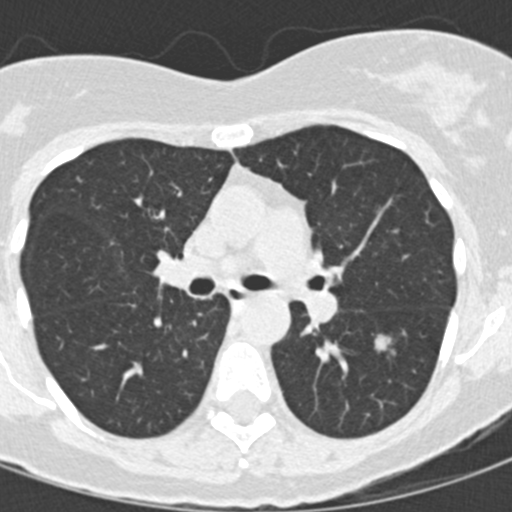
Low-dose screening chest CT, one axial slice; position 89 of 145 along the scan axis; reconstruction kernel B30f; 120 kVp; lung window (W 1500 / L -600 HU); 2 mm slice thickness; 512 × 512 image matrix, field of view 270 × 270 mm.
Outlined on this slice (manually delineated by an expert):
- lesion 1 (tumor, lower lobe of left lung): bounding box <375,334,391,351> (left, top, right, bottom; pixels)